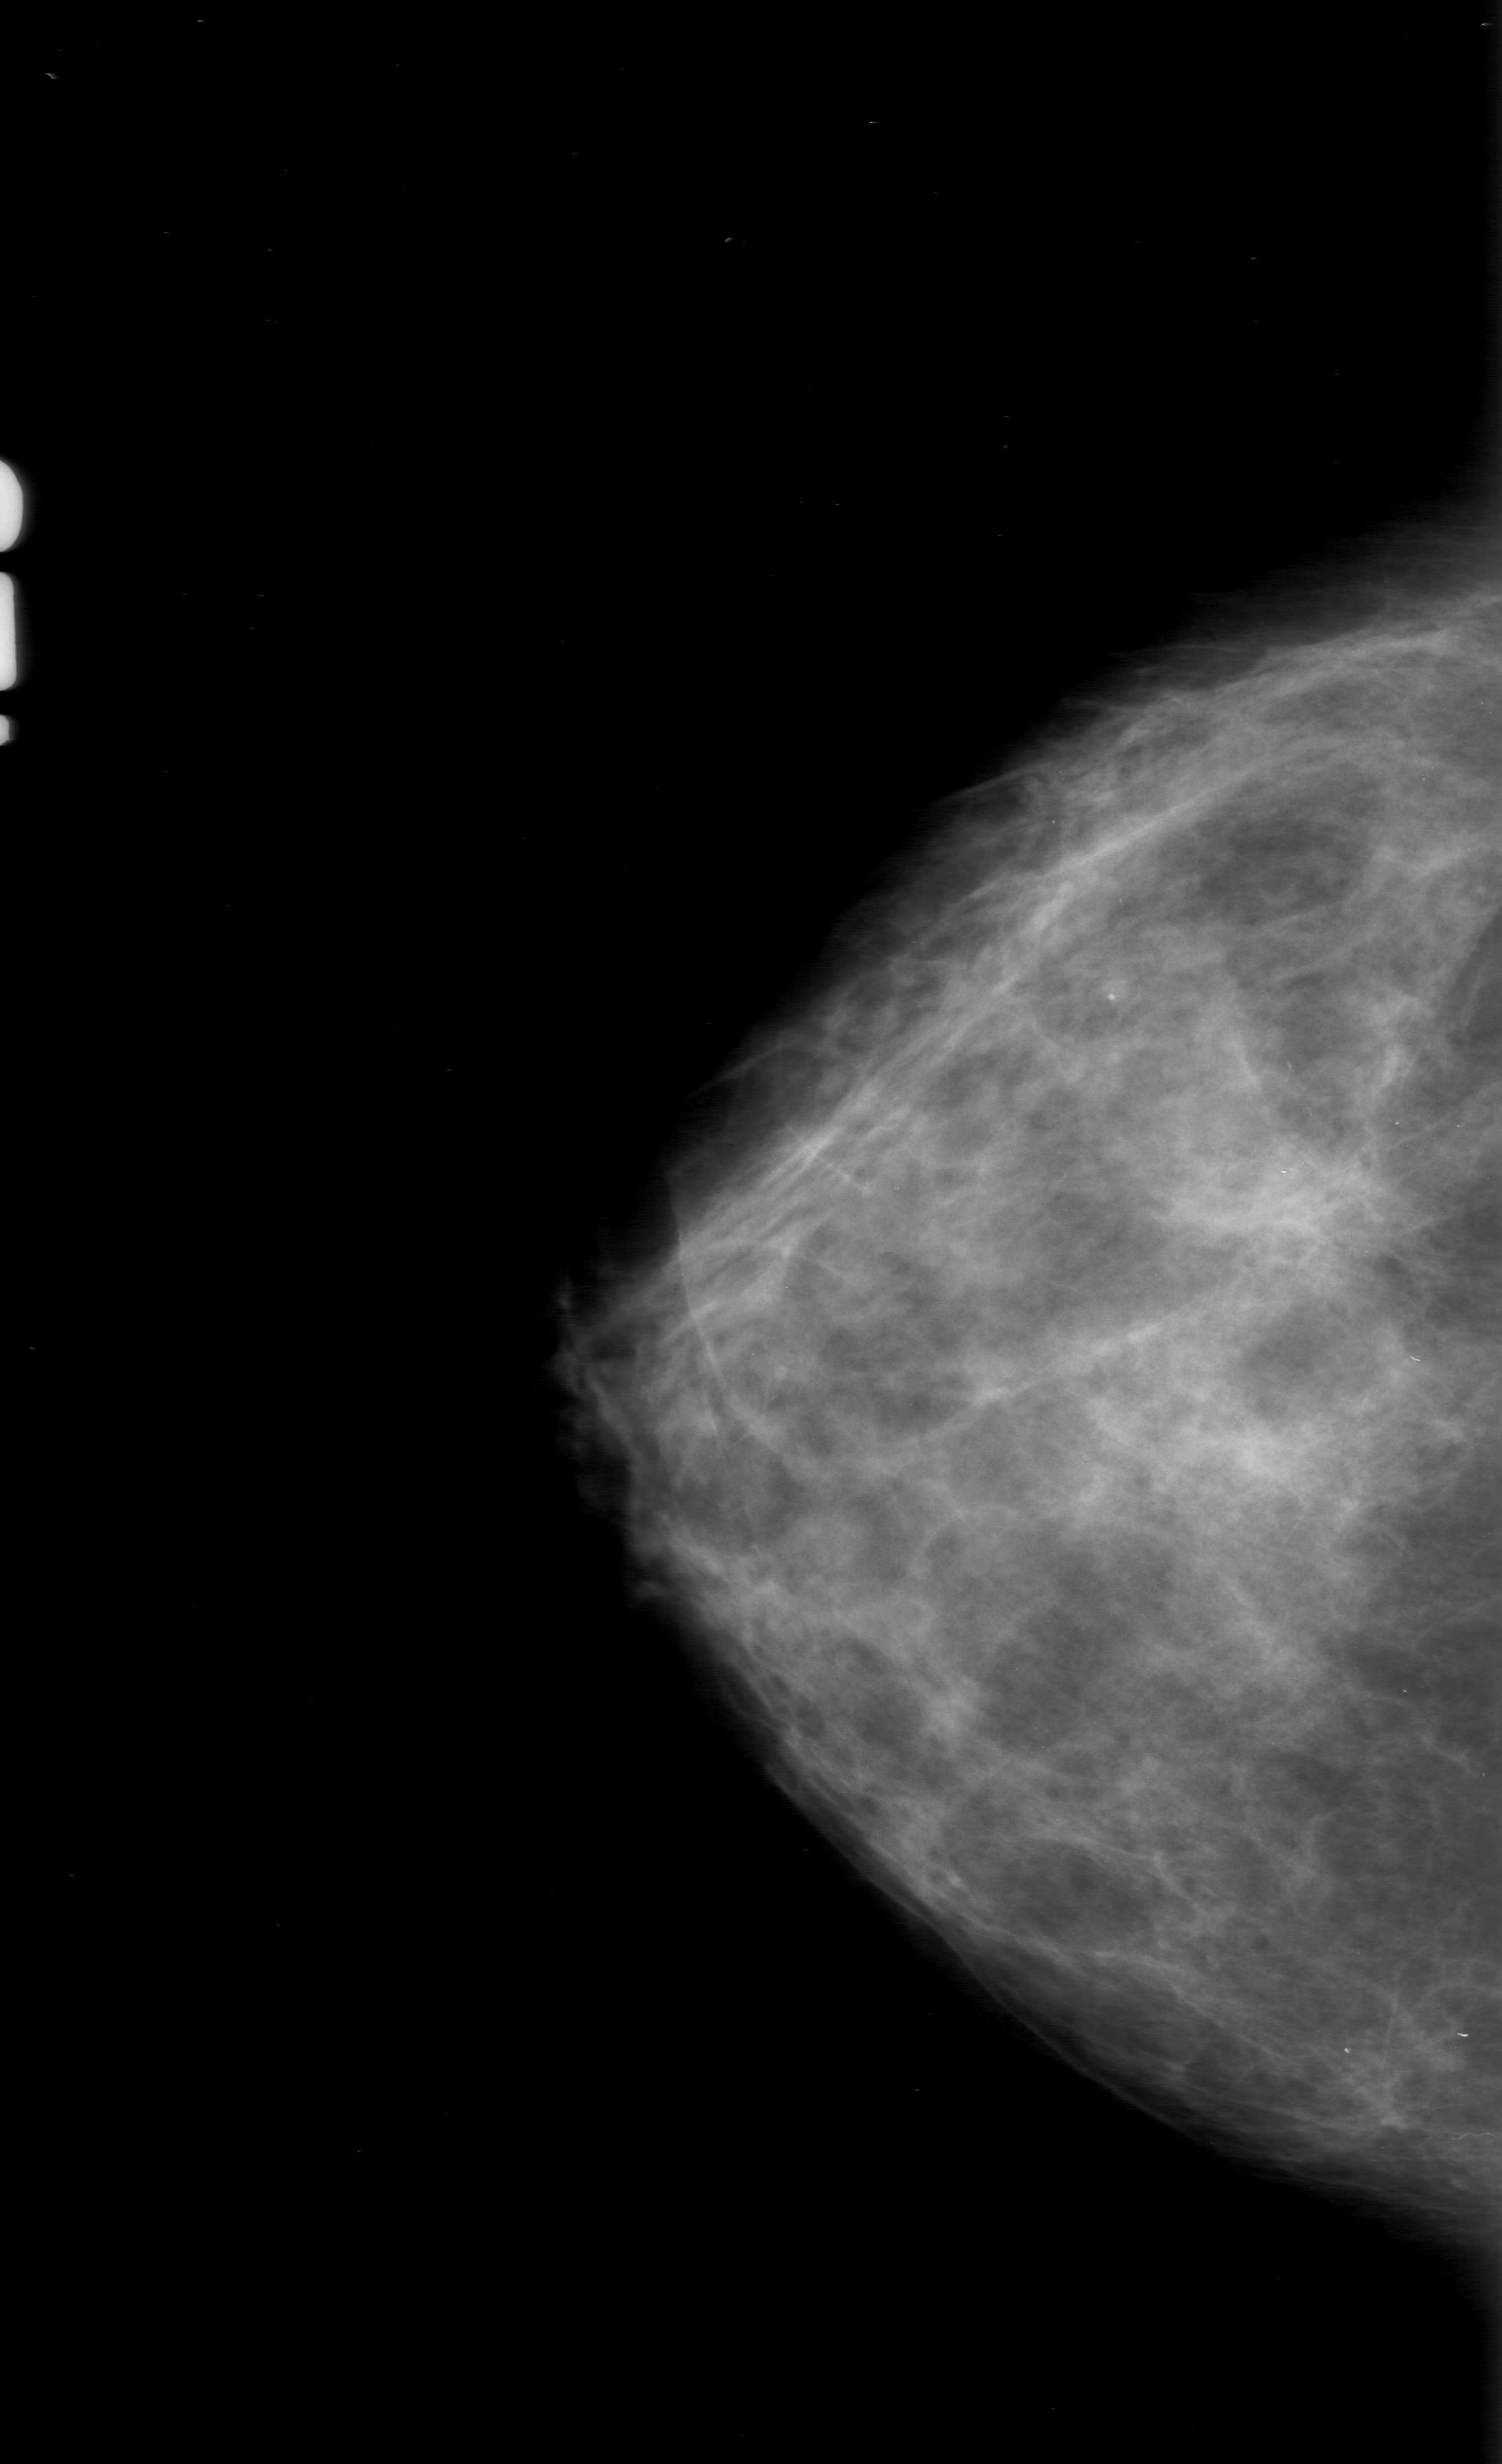
Digitized screen-film mammogram; right breast; craniocaudal (CC) view; 1502 × 2464 image matrix.
Marked abnormalities (boxes around the expert regions of interest):
- calcifications, morphology punctate, distribution clustered; BI-RADS assessment category 0 (incomplete: needs additional imaging); subtlety rating 2 on a 1 (subtle) to 5 (obvious) scale; pathology result (as recorded, not read from the image): malignant: bounding box [x1, y1, x2, y2] px = [1221, 1002, 1404, 1202]